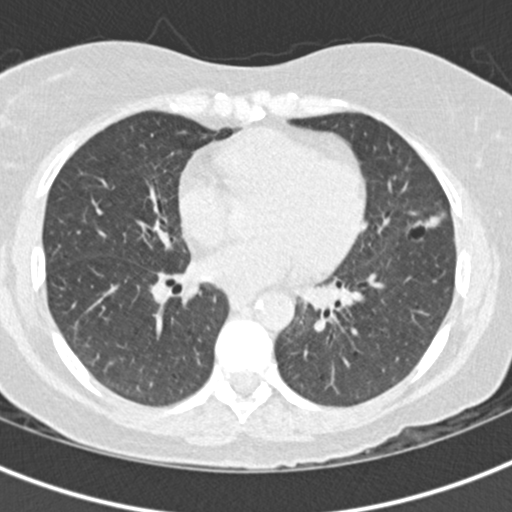
Low-dose screening chest CT, one axial slice; position 80 of 156 along the scan axis; reconstruction kernel B30f; lung window (W 1500 / L -600 HU); 2 mm slice thickness; 512 × 512 image matrix, field of view 298 × 298 mm.
Annotated regions visible in this slice (manually delineated by an expert):
- lesion 1 (tumor, lingular bronchus): bounding box (x1, y1, x2, y2) in pixels: (414, 214, 440, 228)